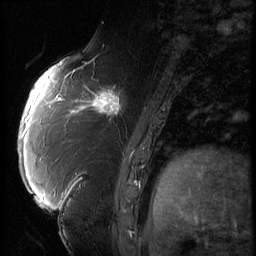
Breast MRI (dynamic contrast-enhanced), one sagittal slice; slice 24 of 66 in the series (ordered by position); 3 images stored at this slice position (order not interpretable as contrast timing); 1.5 T; TE 4.2 ms, TR 9 ms; 256 × 256 image matrix, field of view 180 × 180 mm. Patient: female, 57 years. From the clinical record (not read from this slice): setting: breast cancer imaged before/during neoadjuvant chemotherapy; receptor status: triple-negative.
Structures marked on this image (semi-automatic segmentation, software-assisted and operator-edited):
- analysis volume of interest (the breast-tissue region the enhancement analysis was run in; not a lesion): bounding box <86,74,138,129> (left, top, right, bottom; pixels)
- tumour enhancement mask (voxels above the 140 % enhancement threshold inside the analysis volume of interest): <86,80,126,123>